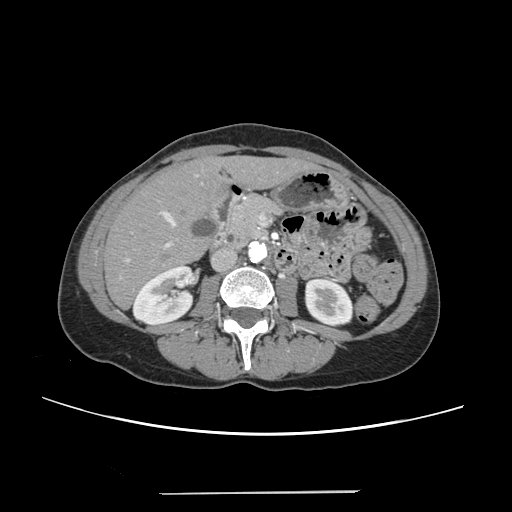
Contrast-enhanced abdominal CT, one axial slice; slice 99 of 240 in the series (ordered by position); soft-tissue window (W 400 / L 40 HU); 1.25 mm slice thickness; 512 × 512 image matrix. Female patient, age 60 years. Case-level facts recorded for this patient, not image findings: diagnosis: colorectal cancer liver metastases, imaged before liver resection; multiple liver metastases: no.
Annotated regions visible in this slice (expert manual segmentation):
- liver: bounding box [x1, y1, x2, y2] px = [105, 158, 307, 308]
- planned liver remnant (the part of the liver to remain after resection): [105, 159, 307, 308]
- portal vein (with intrahepatic branches): [123, 174, 214, 263]